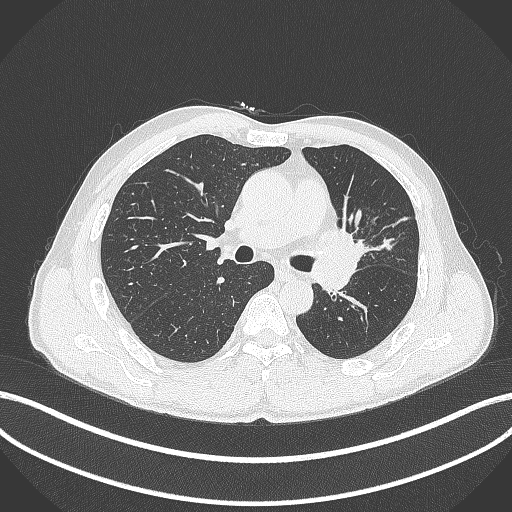
Chest CT, one axial slice; position 252 of 429 along the scan axis; lung window (W 1500 / L -600 HU); 512 × 512 image matrix. Male patient, age 57 years. Case-level facts recorded for this patient, not image findings: clinical TNM (as recorded): T2b N0 M0.
Structures marked on this image (rectangle marked by the reading radiologist):
- lung tumour (recorded histology: squamous cell carcinoma): bounding box <319,220,372,263> (left, top, right, bottom; pixels)